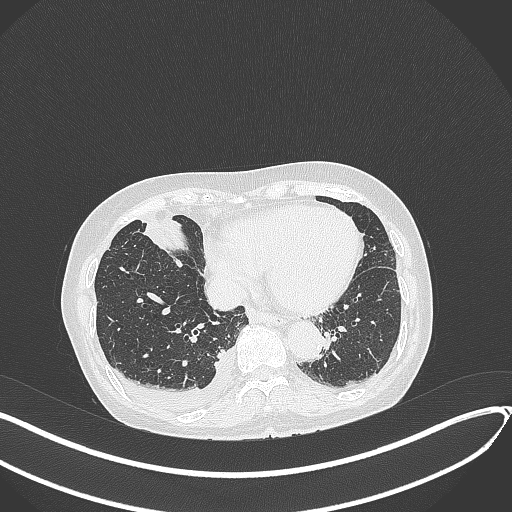
Chest CT, one axial slice; slice 115 of 418 in the series (ordered by position); reconstruction kernel B70f; lung window (W 1500 / L -600 HU); 512 × 512 image matrix, field of view 400 × 400 mm. Female patient, age 75 years. From the clinical record (not read from this slice): clinical TNM (as recorded): T2a N3 M0.
Structures marked on this image (bounding box drawn by a radiologist):
- lung tumour (recorded histology: adenocarcinoma): bounding box (x1, y1, x2, y2) in pixels: (139, 218, 194, 256)